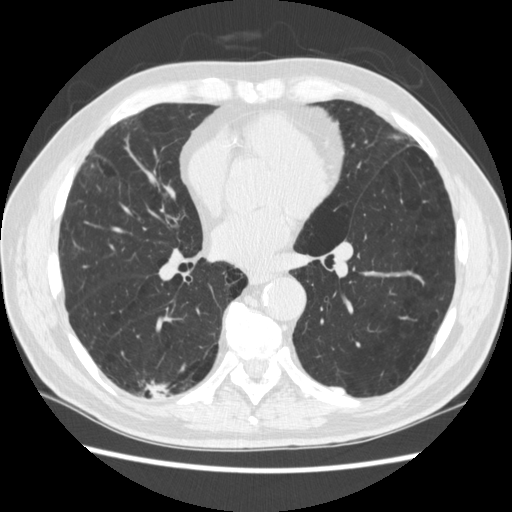
Low-dose screening chest CT, one axial slice; slice 125 of 266 in the series (ordered by position); 120 kVp; lung window (W 1500 / L -600 HU); 1.25 mm slice thickness; 512 × 512 image matrix, field of view 360 × 360 mm.
Outlined on this slice (manually delineated by an expert):
- lesion 1 (tumor, upper lobe of right lung): bounding box [x1, y1, x2, y2] px = [149, 384, 166, 399]